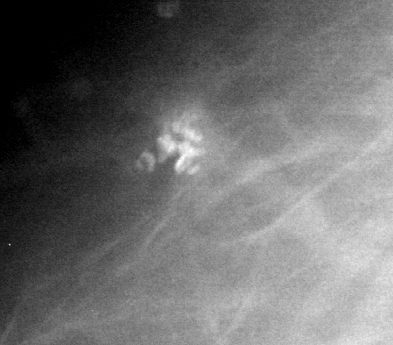
Cropped region of a digitized screen-film mammogram centred on a radiologist-marked abnormality, right breast, MLO view.
Marked abnormality: calcifications, morphology pleomorphic, distribution clustered; BI-RADS assessment category 4; pathology result (as recorded, not read from the image): benign.